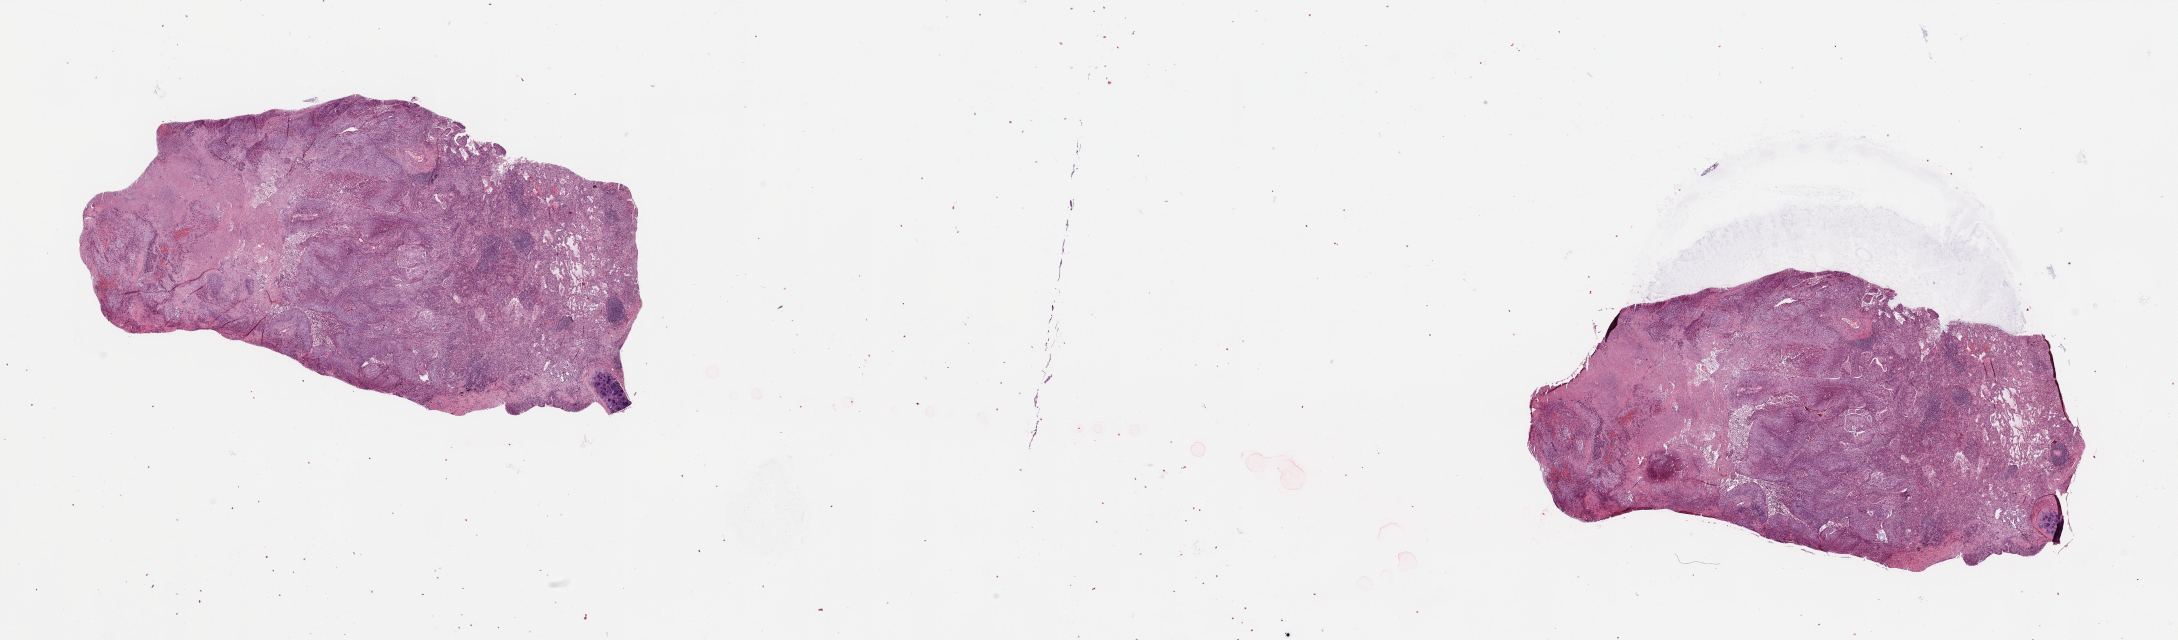
H&E-stained whole-slide image, low-resolution overview of the scanned area, about 34.5 x 10.1 mm (from a 20x scan). Tumour tissue sample, lung. Patient: male, age 53 years. Histologic grade: G2 (moderately differentiated).
- diagnosis: Squamous cell carcinoma, NOS
- AJCC pathologic stage: IIIA